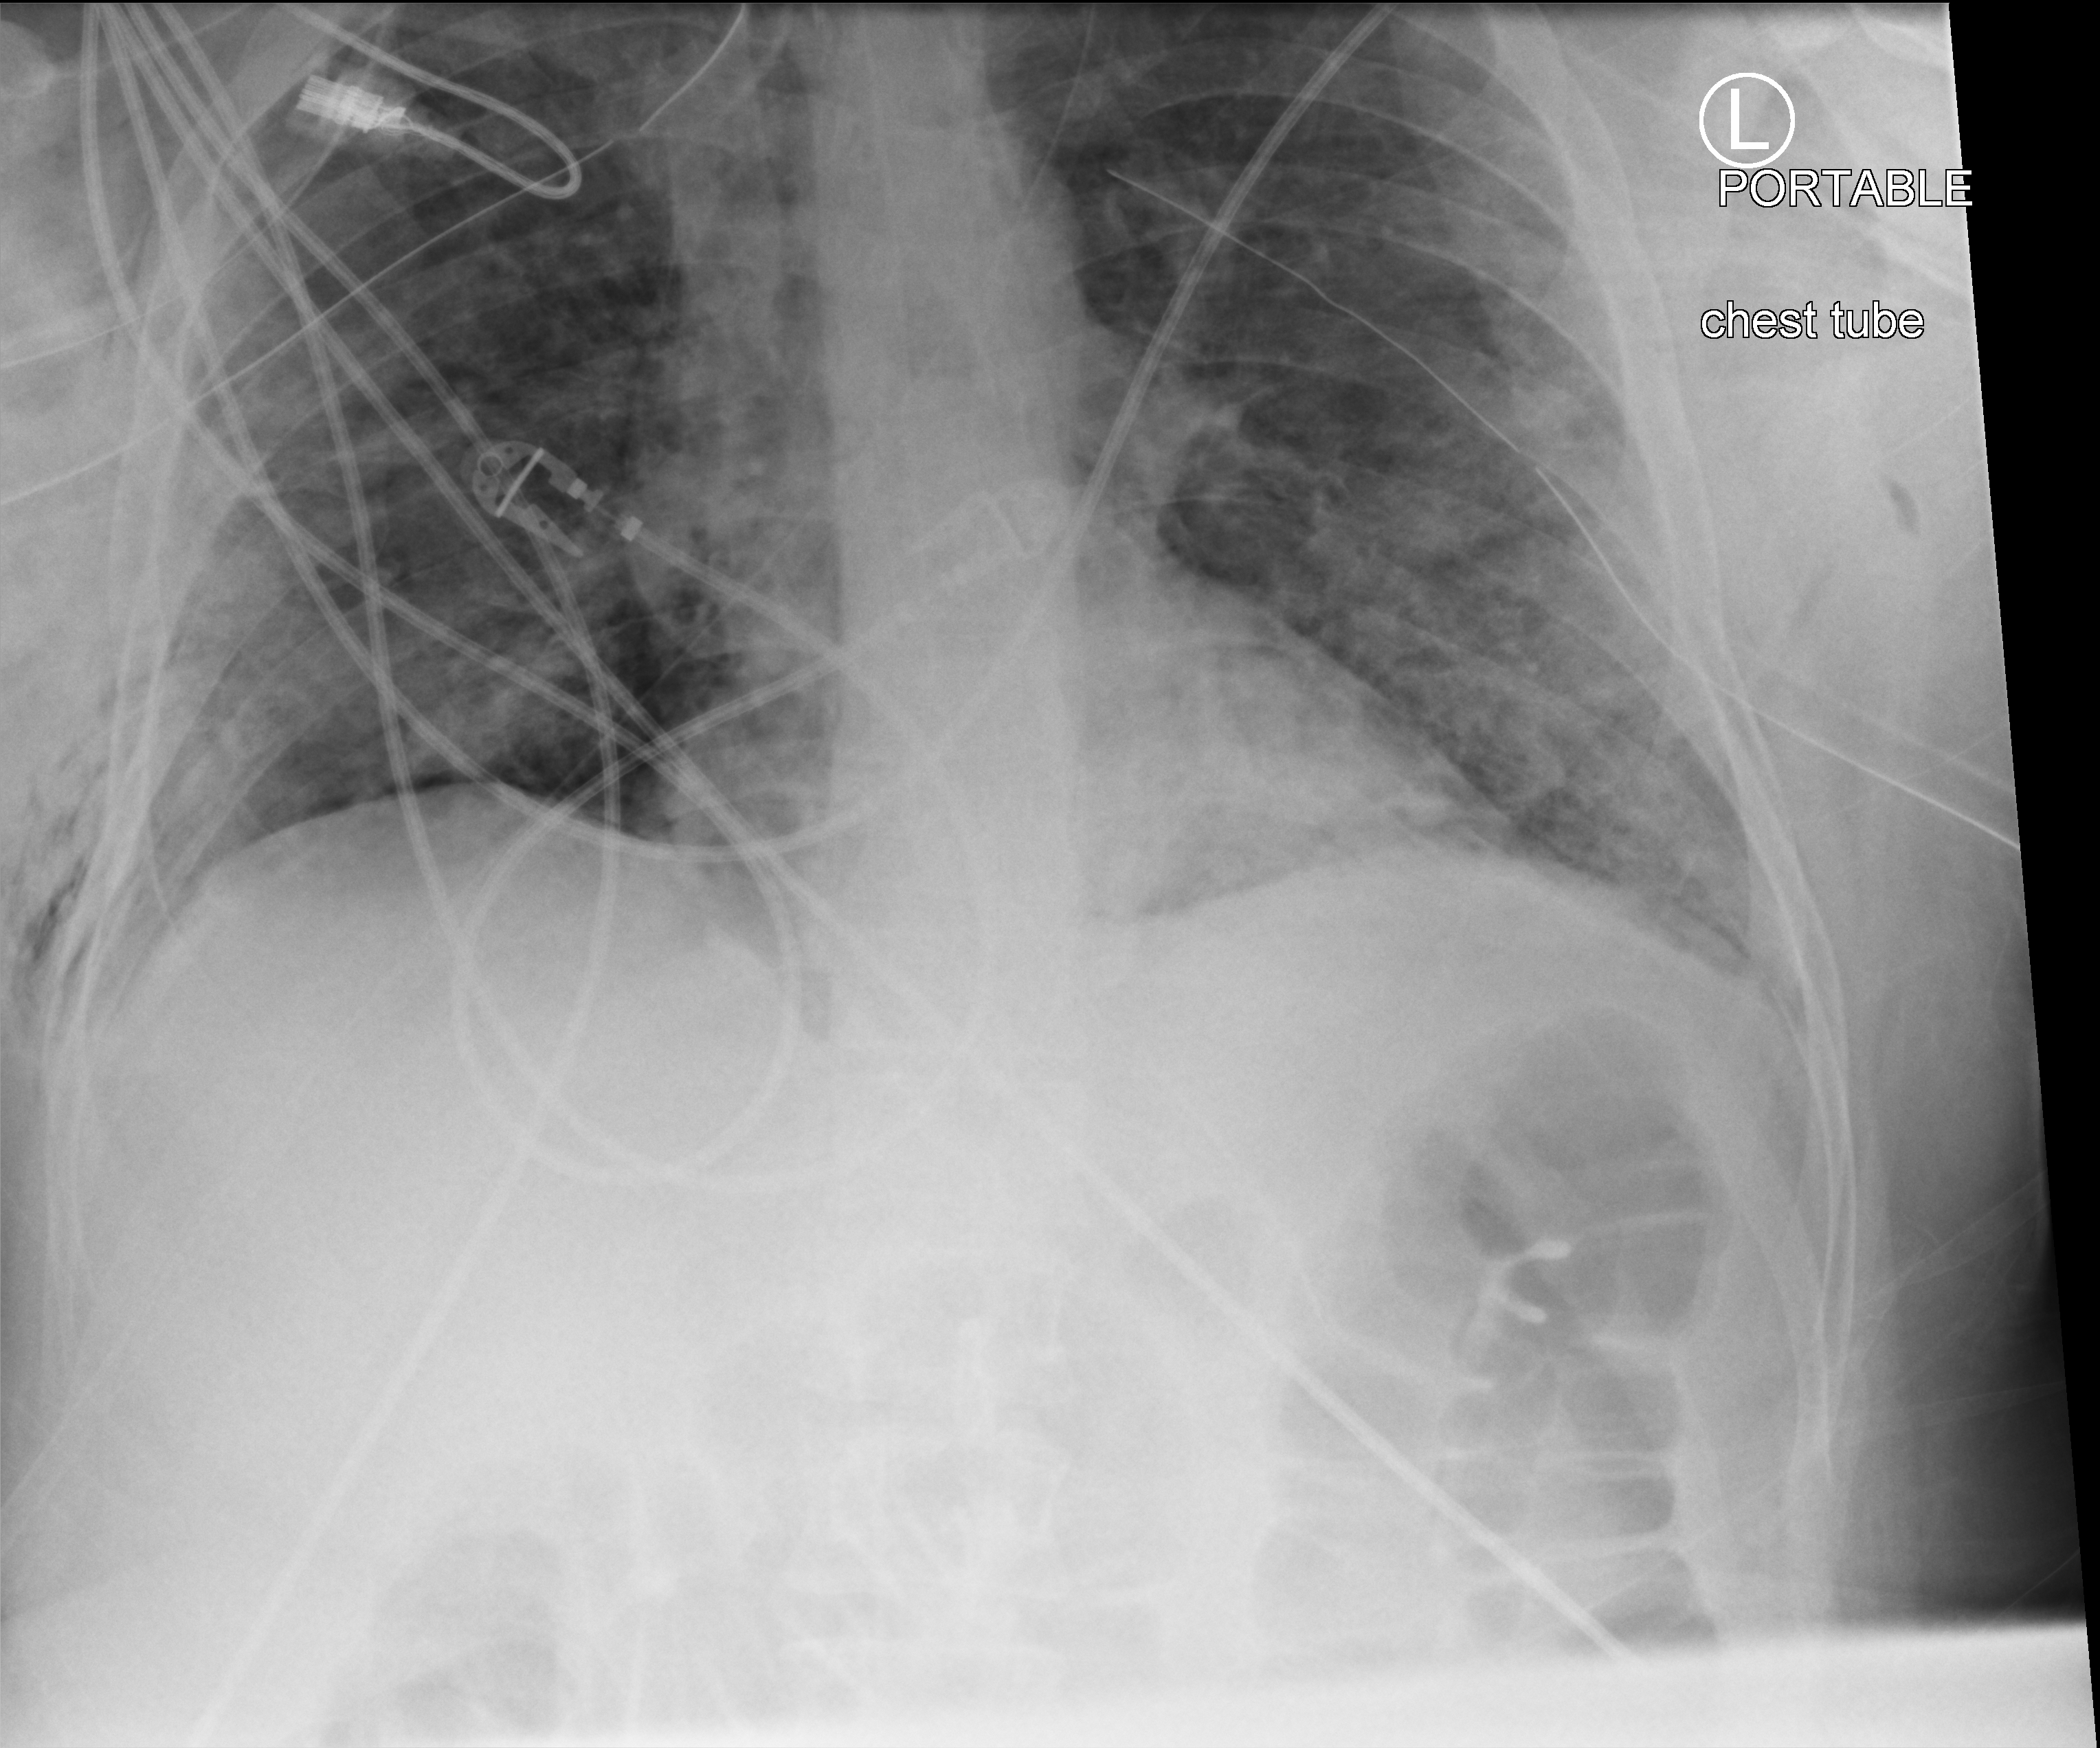
Portable chest radiograph; anteroposterior (AP) projection. Patient hospitalised with COVID-19; male, aged 18–59 years.
Hospital-stay facts (about this admission, not read from this image; timing relative to this image not recorded): mechanically ventilated during this hospital stay: yes; admitted to intensive care during this hospital stay: yes; diabetes (admission record): yes.